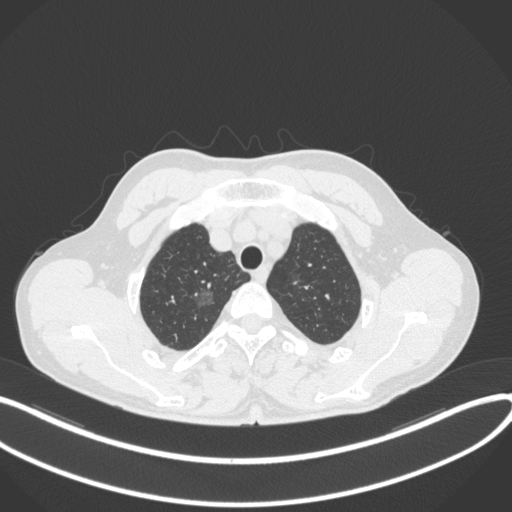
Chest CT, one axial slice. Position 321 of 407 along the scan axis. Reconstruction kernel B31f. 120 kVp. Lung window (W 1500 / L -600 HU). 1 mm slice thickness. 512 × 512 image matrix, field of view 400 × 400 mm. Patient: male, 58 years. Case-level facts recorded for this patient, not image findings: clinical TNM (as recorded): T1c N0 M0.
Outlined on this slice (rectangle marked by the reading radiologist):
- lung tumour (recorded histology: adenocarcinoma): box from (x=188, y=278) to (x=218, y=308) px